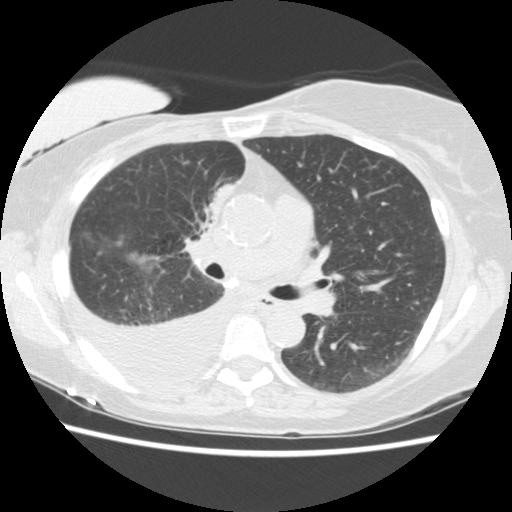
Low-dose screening chest CT, axial slice, third screening round (two years after baseline), lung window (W 1500 / L -600 HU), 2.5 mm slice thickness, standard (soft-tissue) reconstruction kernel (STANDARD), 120 kVp. Female participant, aged 56 years at enrolment. Current smoker at enrolment.
- Expert reader's lesion annotation, box from (x=184, y=171) to (x=248, y=238) px.
- The screening reader recorded 2 non-calcified nodules or masses ≥4 mm on this exam (right middle lobe, right lower lobe); which of them this box marks is not recorded.
- Participant outcome: lung cancer diagnosed 160 days after this screen — adenocarcinoma, NOS, right upper lobe, stage IIIB (AJCC 6th edition), 8 mm at pathology.